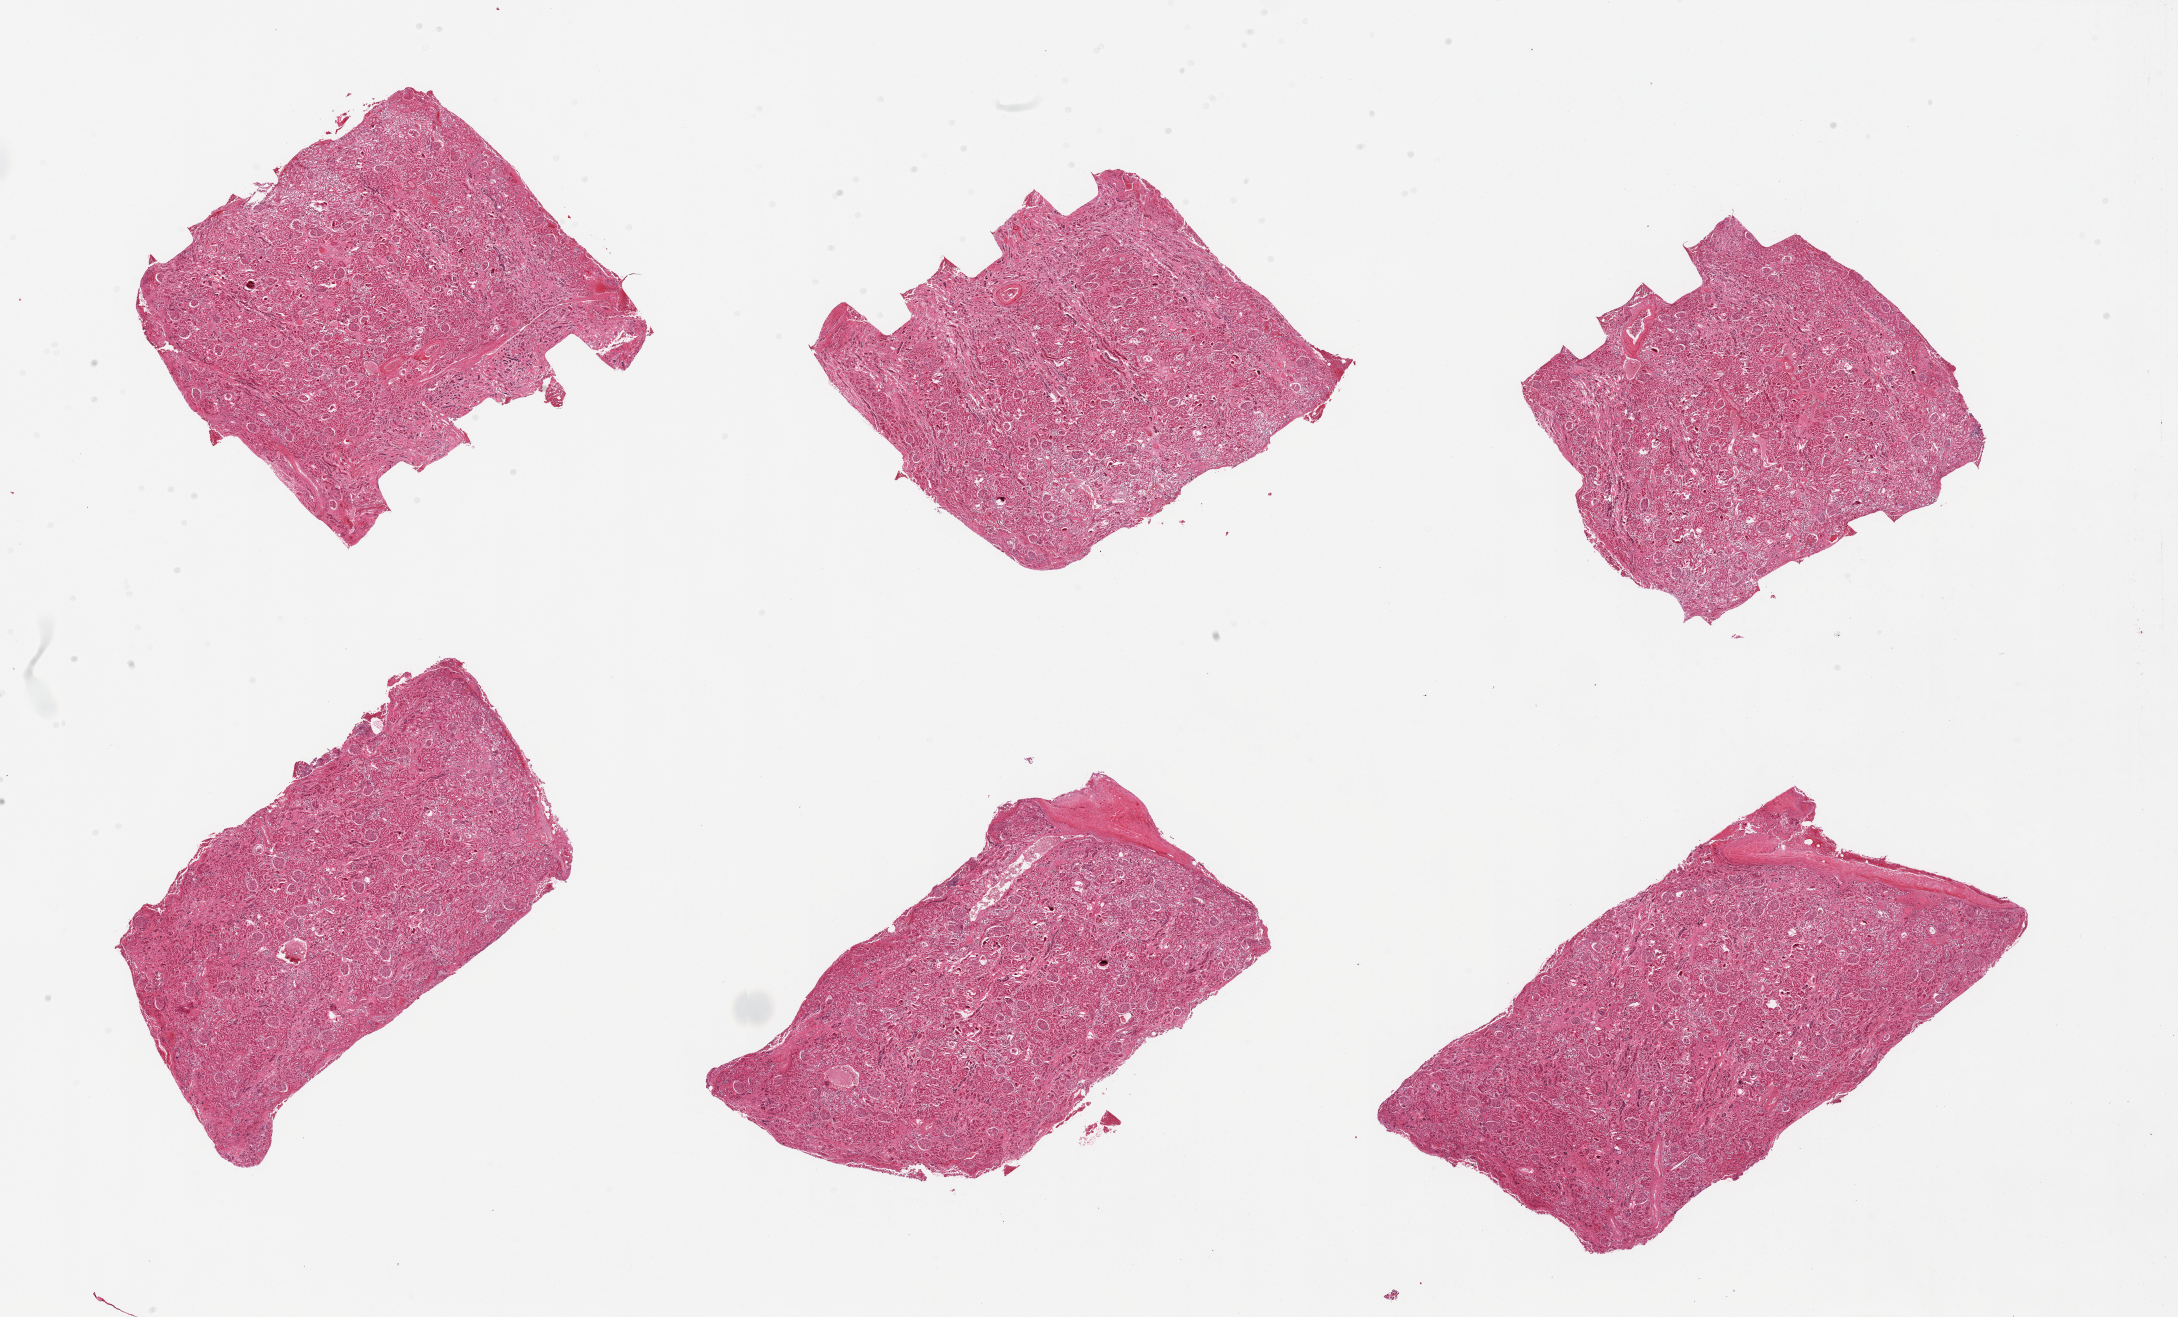
Digitized hematoxylin and eosin (H&E)-stained section, brightfield — whole scanned area (about 34.5 x 20.8 mm, slide scanned at 20x) shown as a low-resolution overview. PAXgene-fixed, paraffin-embedded tissue. Sampled site (target tissue): renal cortex. Tissue donor sample. Donor sex: male.
Reviewer comment on this tissue sample: 6 pieces, all sections contain glomeruli, few sclerotic.